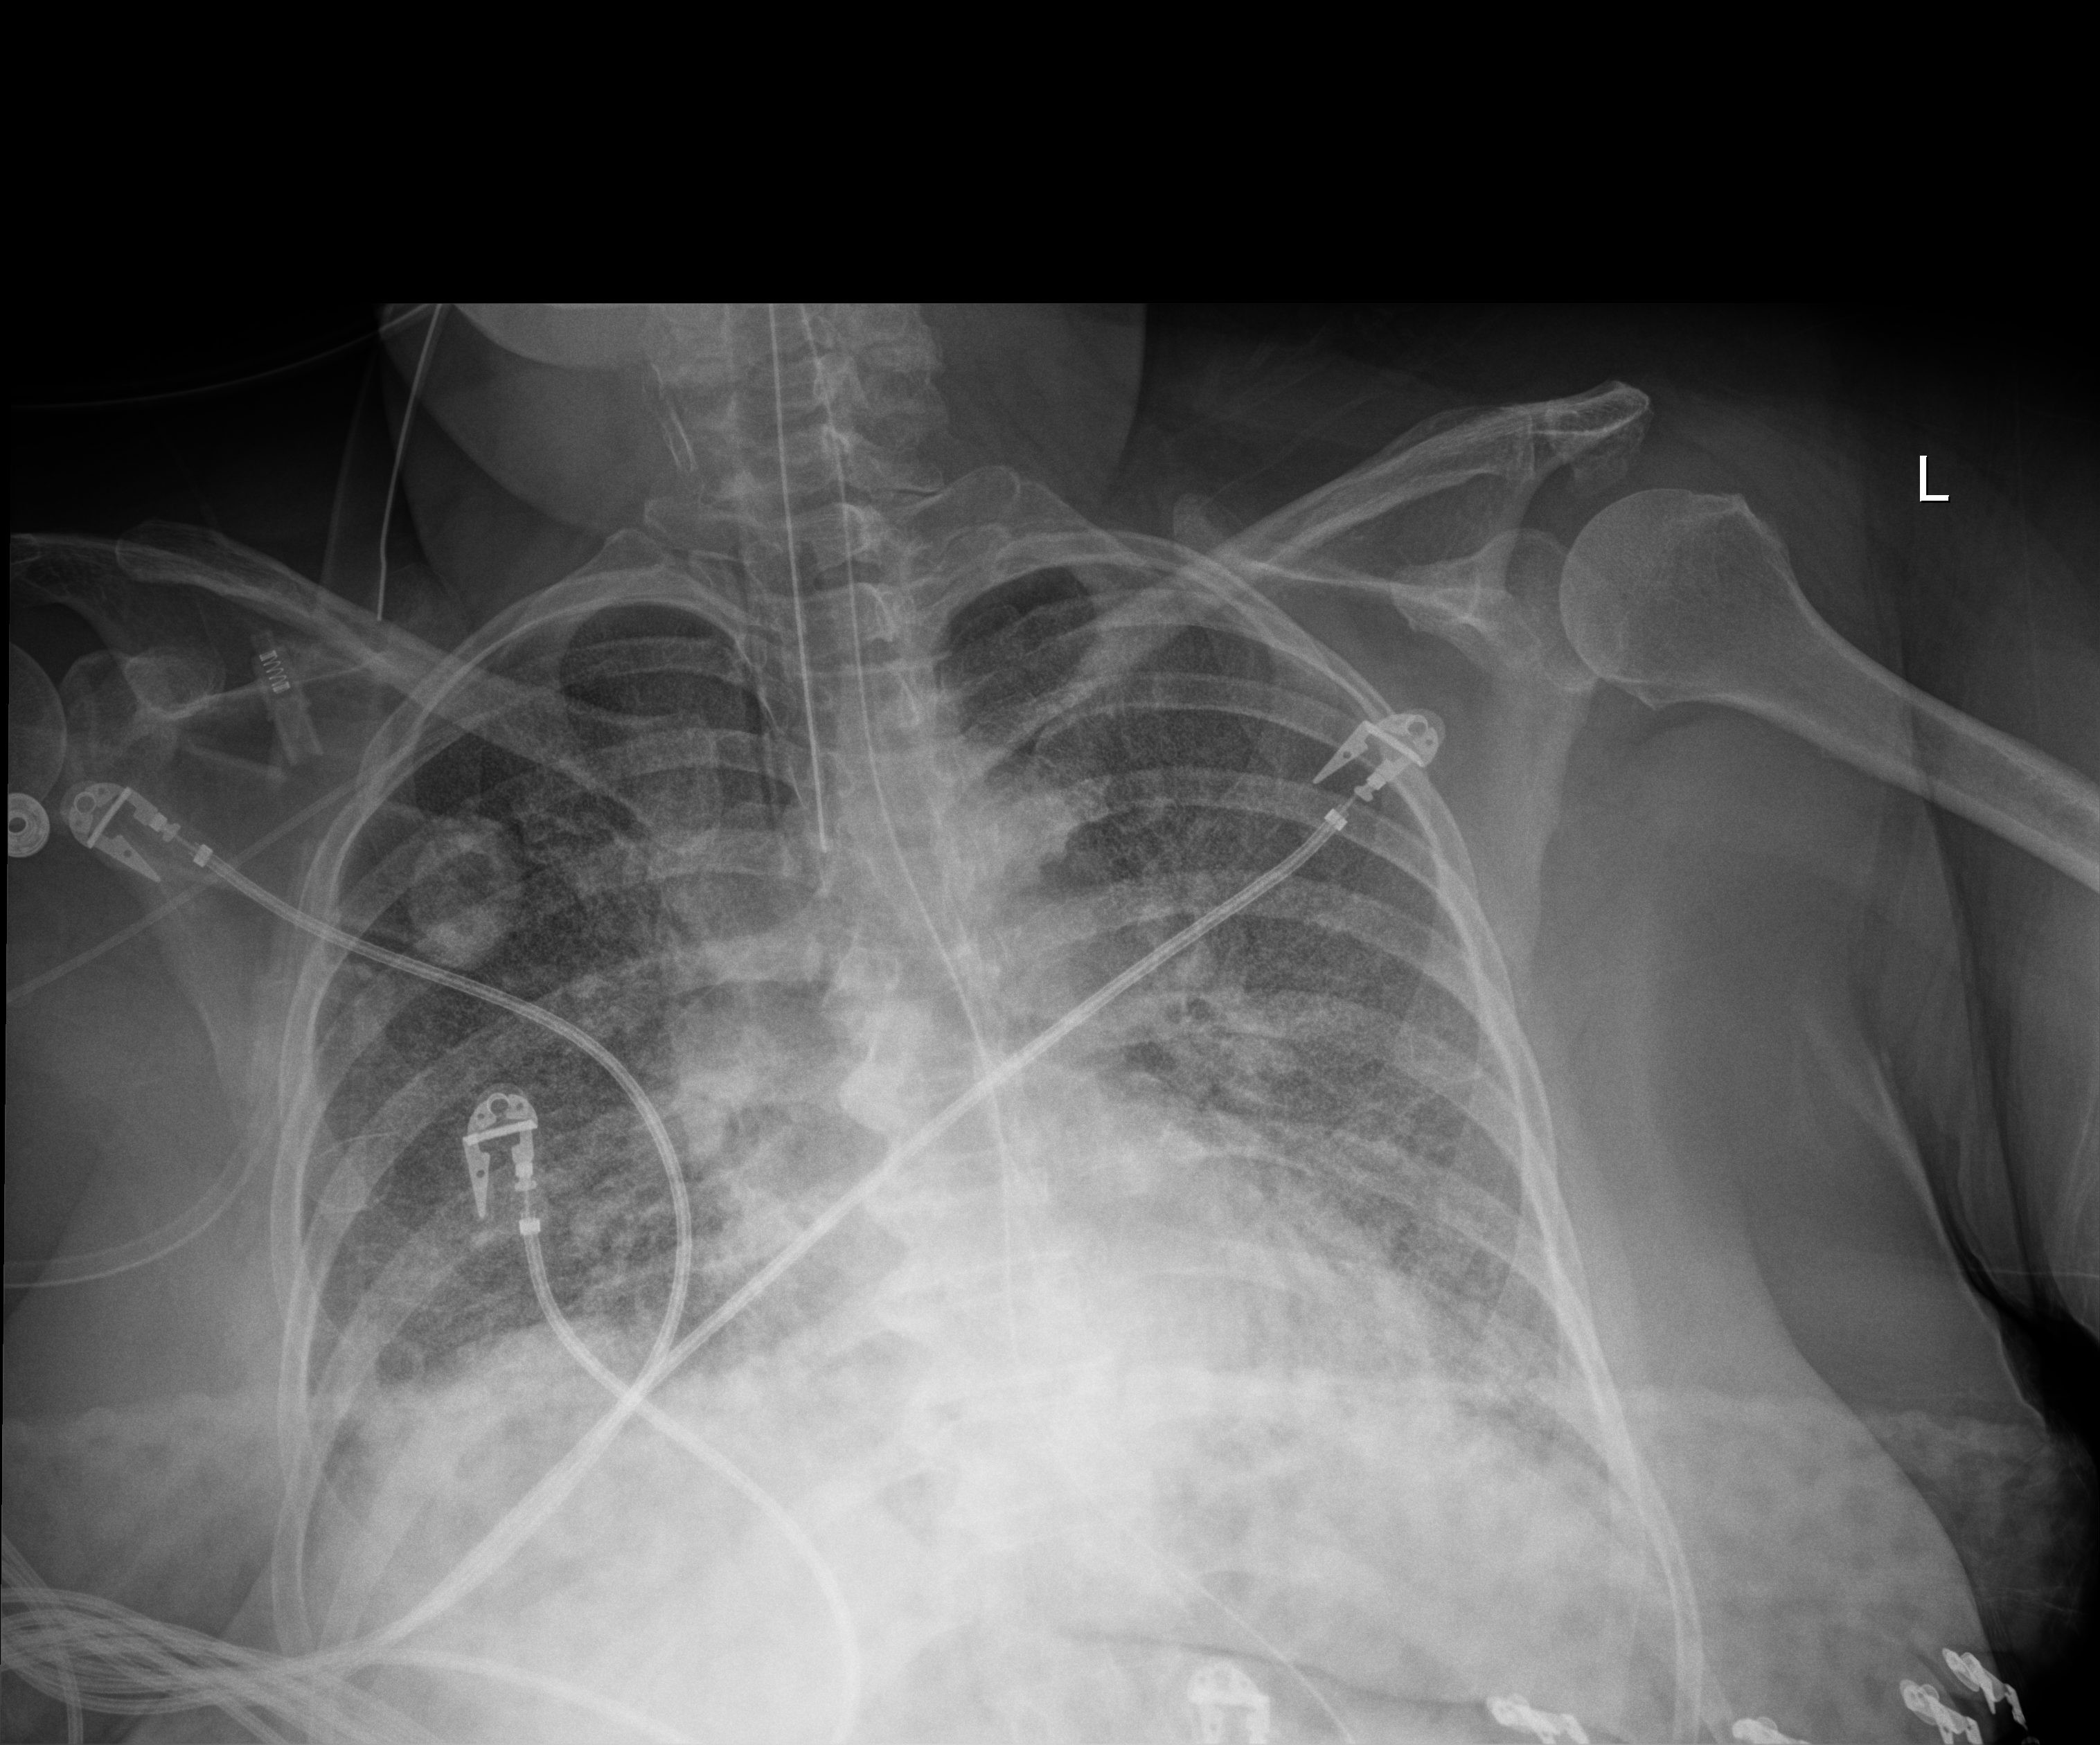
Chest radiograph (digital radiography). Patient hospitalised with COVID-19; female, aged 60–74 years.
From the hospital-stay record, not from the radiograph (when in the stay this image was taken is not recorded): hypertension (admission record): no; length of hospital stay: 38 days.